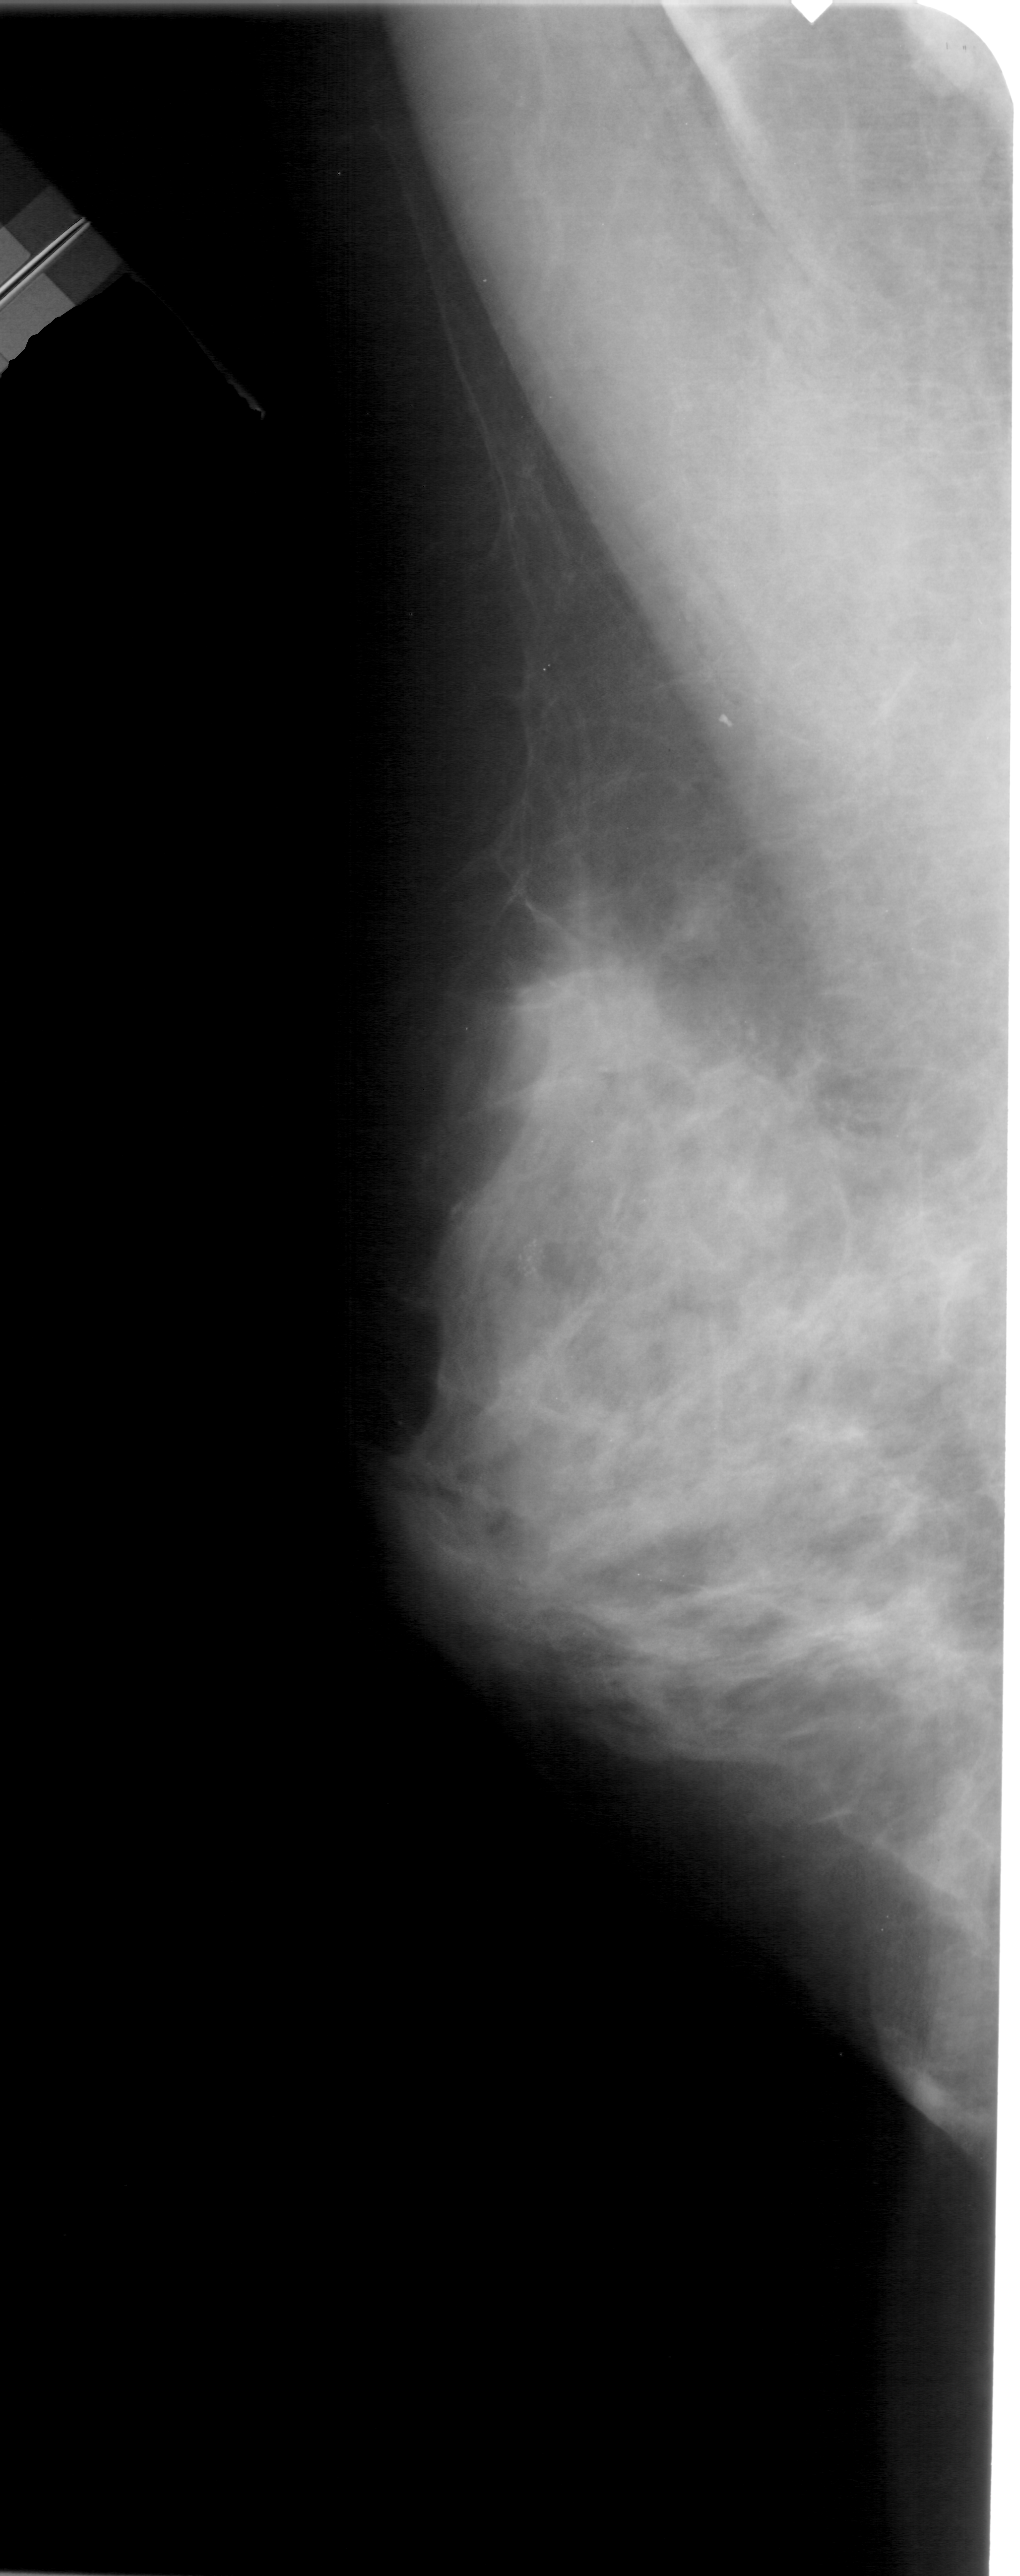
Digitized screen-film mammogram; left breast; mediolateral oblique (MLO) view; breast composition: extremely dense (BI-RADS density category 4 of 4); 1020 × 2576 image matrix.
Expert-marked regions of interest on this image (one box per marked abnormality):
- calcifications, morphology pleomorphic, distribution clustered; BI-RADS assessment category 4; pathology (as recorded): benign: bounding box (x1, y1, x2, y2) in pixels: (507, 1224, 560, 1297)